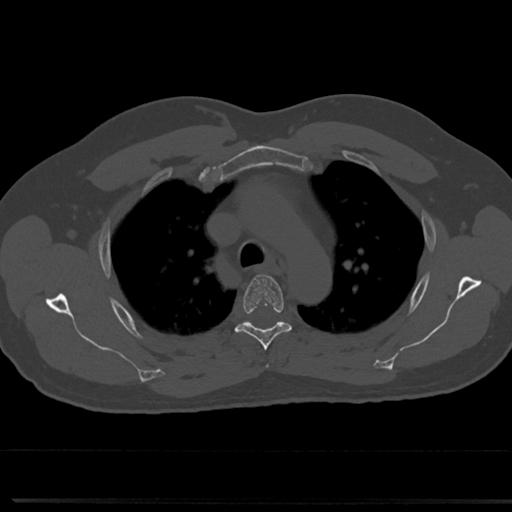
CT including the spine, one axial slice. Slice 545 of 817 in the series (ordered by position). Bone window (W 1800 / L 400 HU). 512 × 512 image matrix, field of view 355 × 355 mm. Patient: male, 61 years. Case-level facts recorded for this patient, not image findings: primary cancer: prostate.
Outlined on this slice (semi-automatically segmented with operator editing):
- T3 vertebra: bounding box [x1, y1, x2, y2] px = [266, 364, 269, 368]
- T4 vertebra: [233, 274, 293, 349]